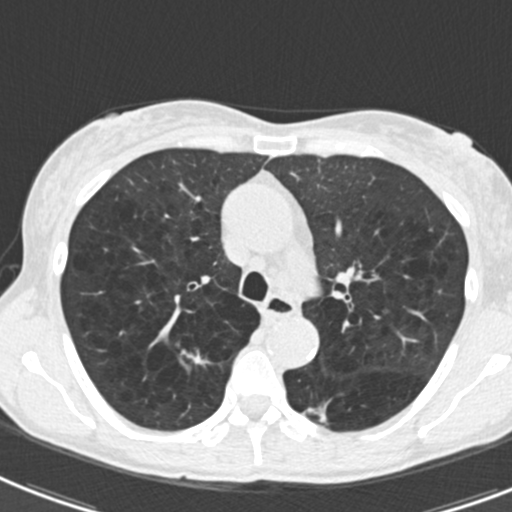
Low-dose screening chest CT, axial slice, second screening round (one year after baseline), lung window (W 1500 / L -600 HU), 2 mm slice thickness, 120 kVp, 512 × 512 image matrix. Female participant, aged 61 years at enrolment. Current smoker at enrolment.
Expert-annotated lung lesion, bounding box <172,336,225,384> (left, top, right, bottom; pixels). Reader record for this screening exam (exam-level; its link to the box is not recorded): non-calcified nodule or mass ≥4 mm, right upper lobe, 12 × 6 mm, smooth margins, soft tissue attenuation, pre-existing on the prior screen: yes; interval growth: yes. Lung cancer was diagnosed 455 days after this screen: non-small cell carcinoma, right upper lobe, undifferentiated (G4), stage IA (AJCC 6th edition), 15 mm at pathology.